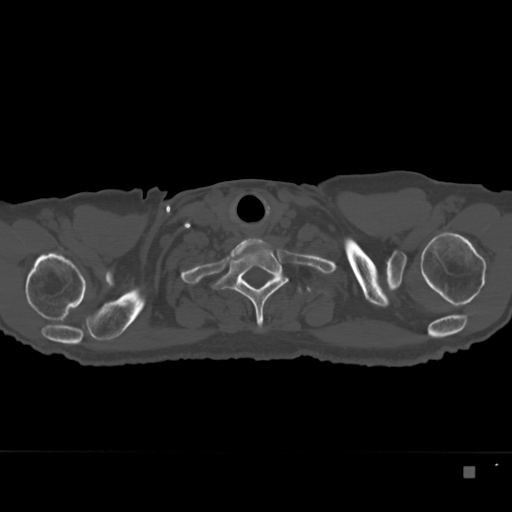
CT including the spine, one axial slice. Position 316 of 332 along the scan axis. Bone window (W 1800 / L 400 HU). 1.5 mm slice thickness. 512 × 512 image matrix, field of view 389 × 389 mm. Male patient, age 72 years. Case-level facts recorded for this patient, not image findings: primary cancer: skeletal.
Outlined on this slice (semi-automatically segmented with operator editing):
- T1 vertebra: bounding box <214,239,288,330> (left, top, right, bottom; pixels)
- T2 vertebra: <247,283,302,294>